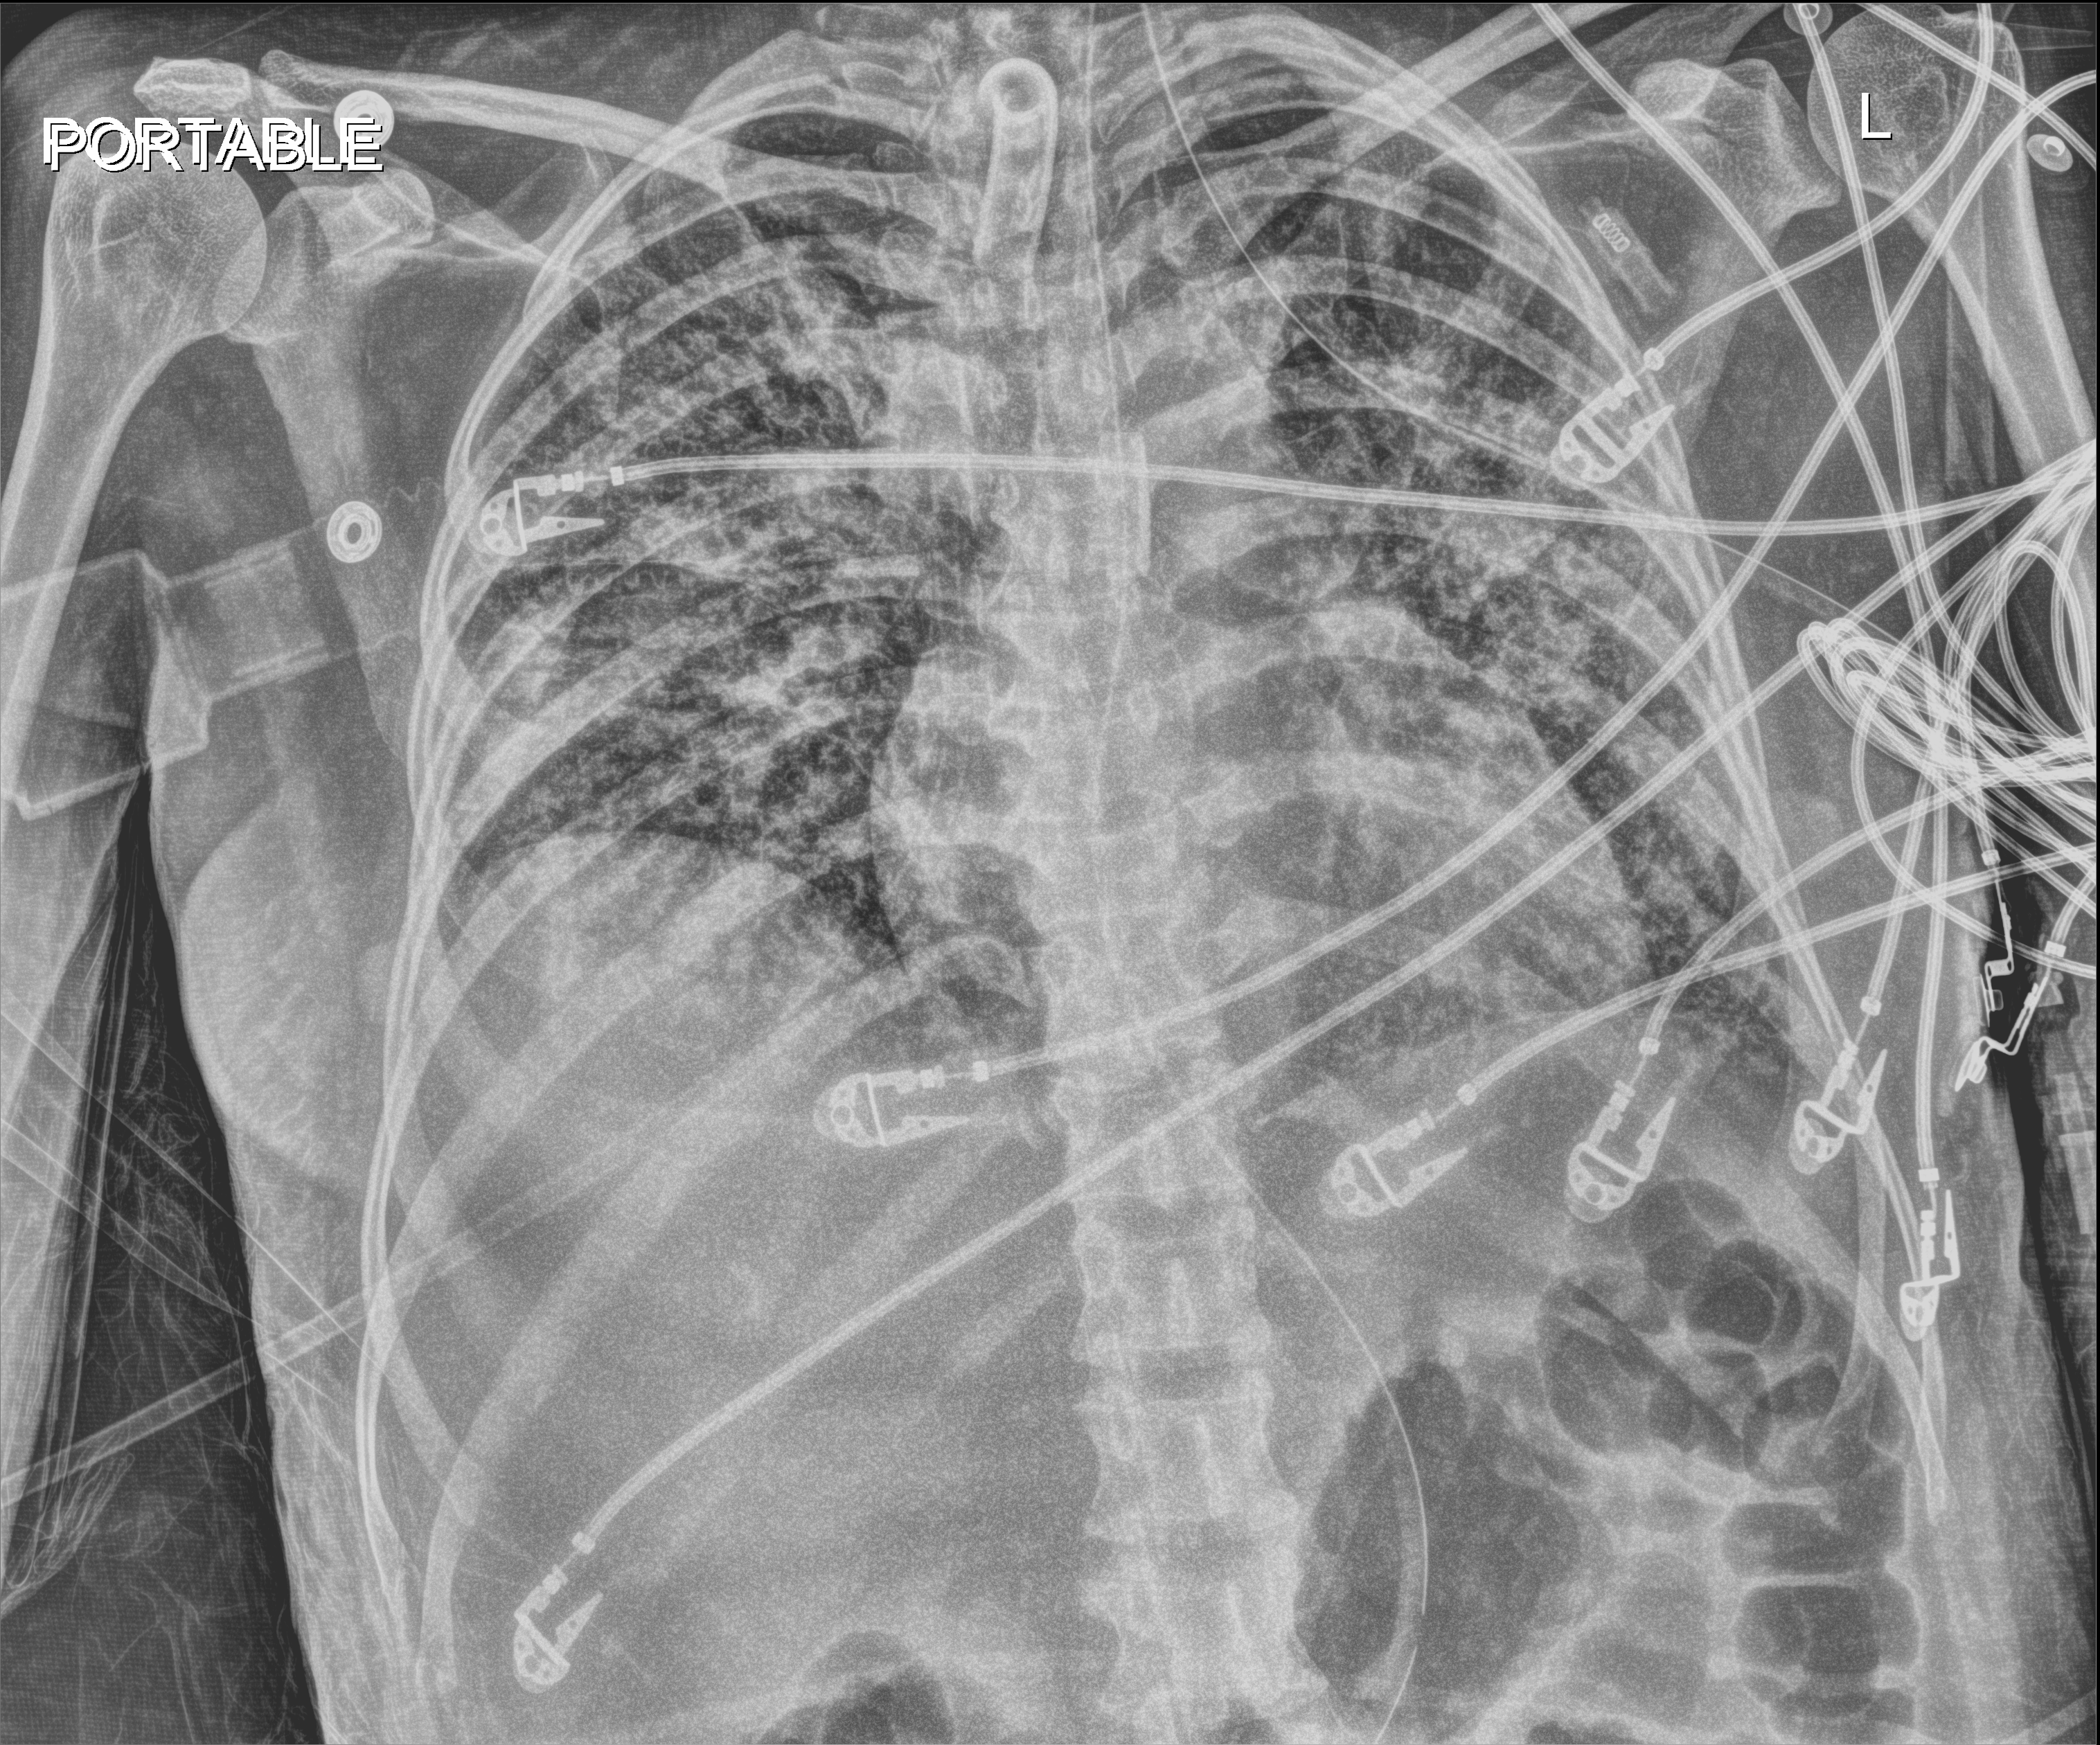
Chest X-ray (portable); anteroposterior (AP) projection. Patient hospitalised with COVID-19; female, aged 18–59 years.
Admission-level facts for this patient (not findings on this image; timing relative to this image not recorded): admitted to intensive care during this hospital stay: yes; mechanically ventilated during this hospital stay: yes.